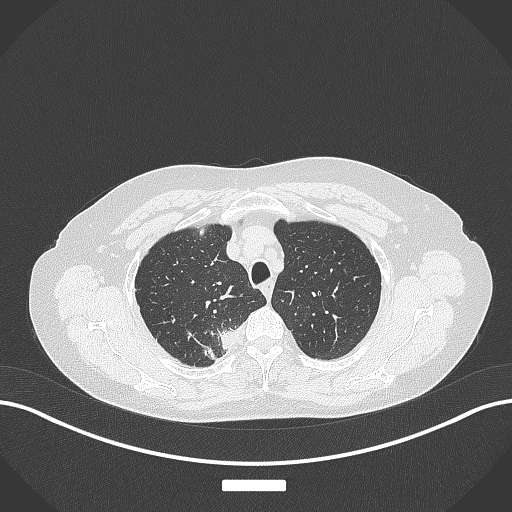
Chest CT, one axial slice. Slice 320 of 357 in the series (ordered by position). Reconstruction kernel B70f. 120 kVp. Lung window (W 1500 / L -600 HU). 1 mm slice thickness. 512 × 512 image matrix, field of view 400 × 400 mm. Female patient, age 62 years. From the clinical record (not read from this slice): clinical TNM (as recorded): T1c N1 M0.
Annotated regions visible in this slice (bounding box drawn by a radiologist):
- lung tumour (recorded histology: squamous cell carcinoma): bounding box <214,322,240,353> (left, top, right, bottom; pixels)